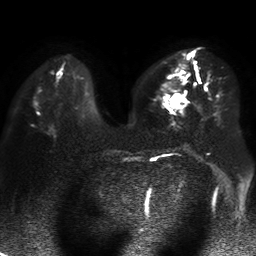
Breast MRI, one axial slice. Position 21 of 50 along the scan axis. Diffusion-weighted series; image 2 of 4 stored at this slice position (different b-values; order by instance number). 1.5 T. 4 mm slice thickness. 256 × 256 image matrix. Female patient.
Outlined on this slice (expert manual segmentation):
- tumour on diffusion-weighted imaging: bounding box [x1, y1, x2, y2] px = [171, 94, 185, 108]